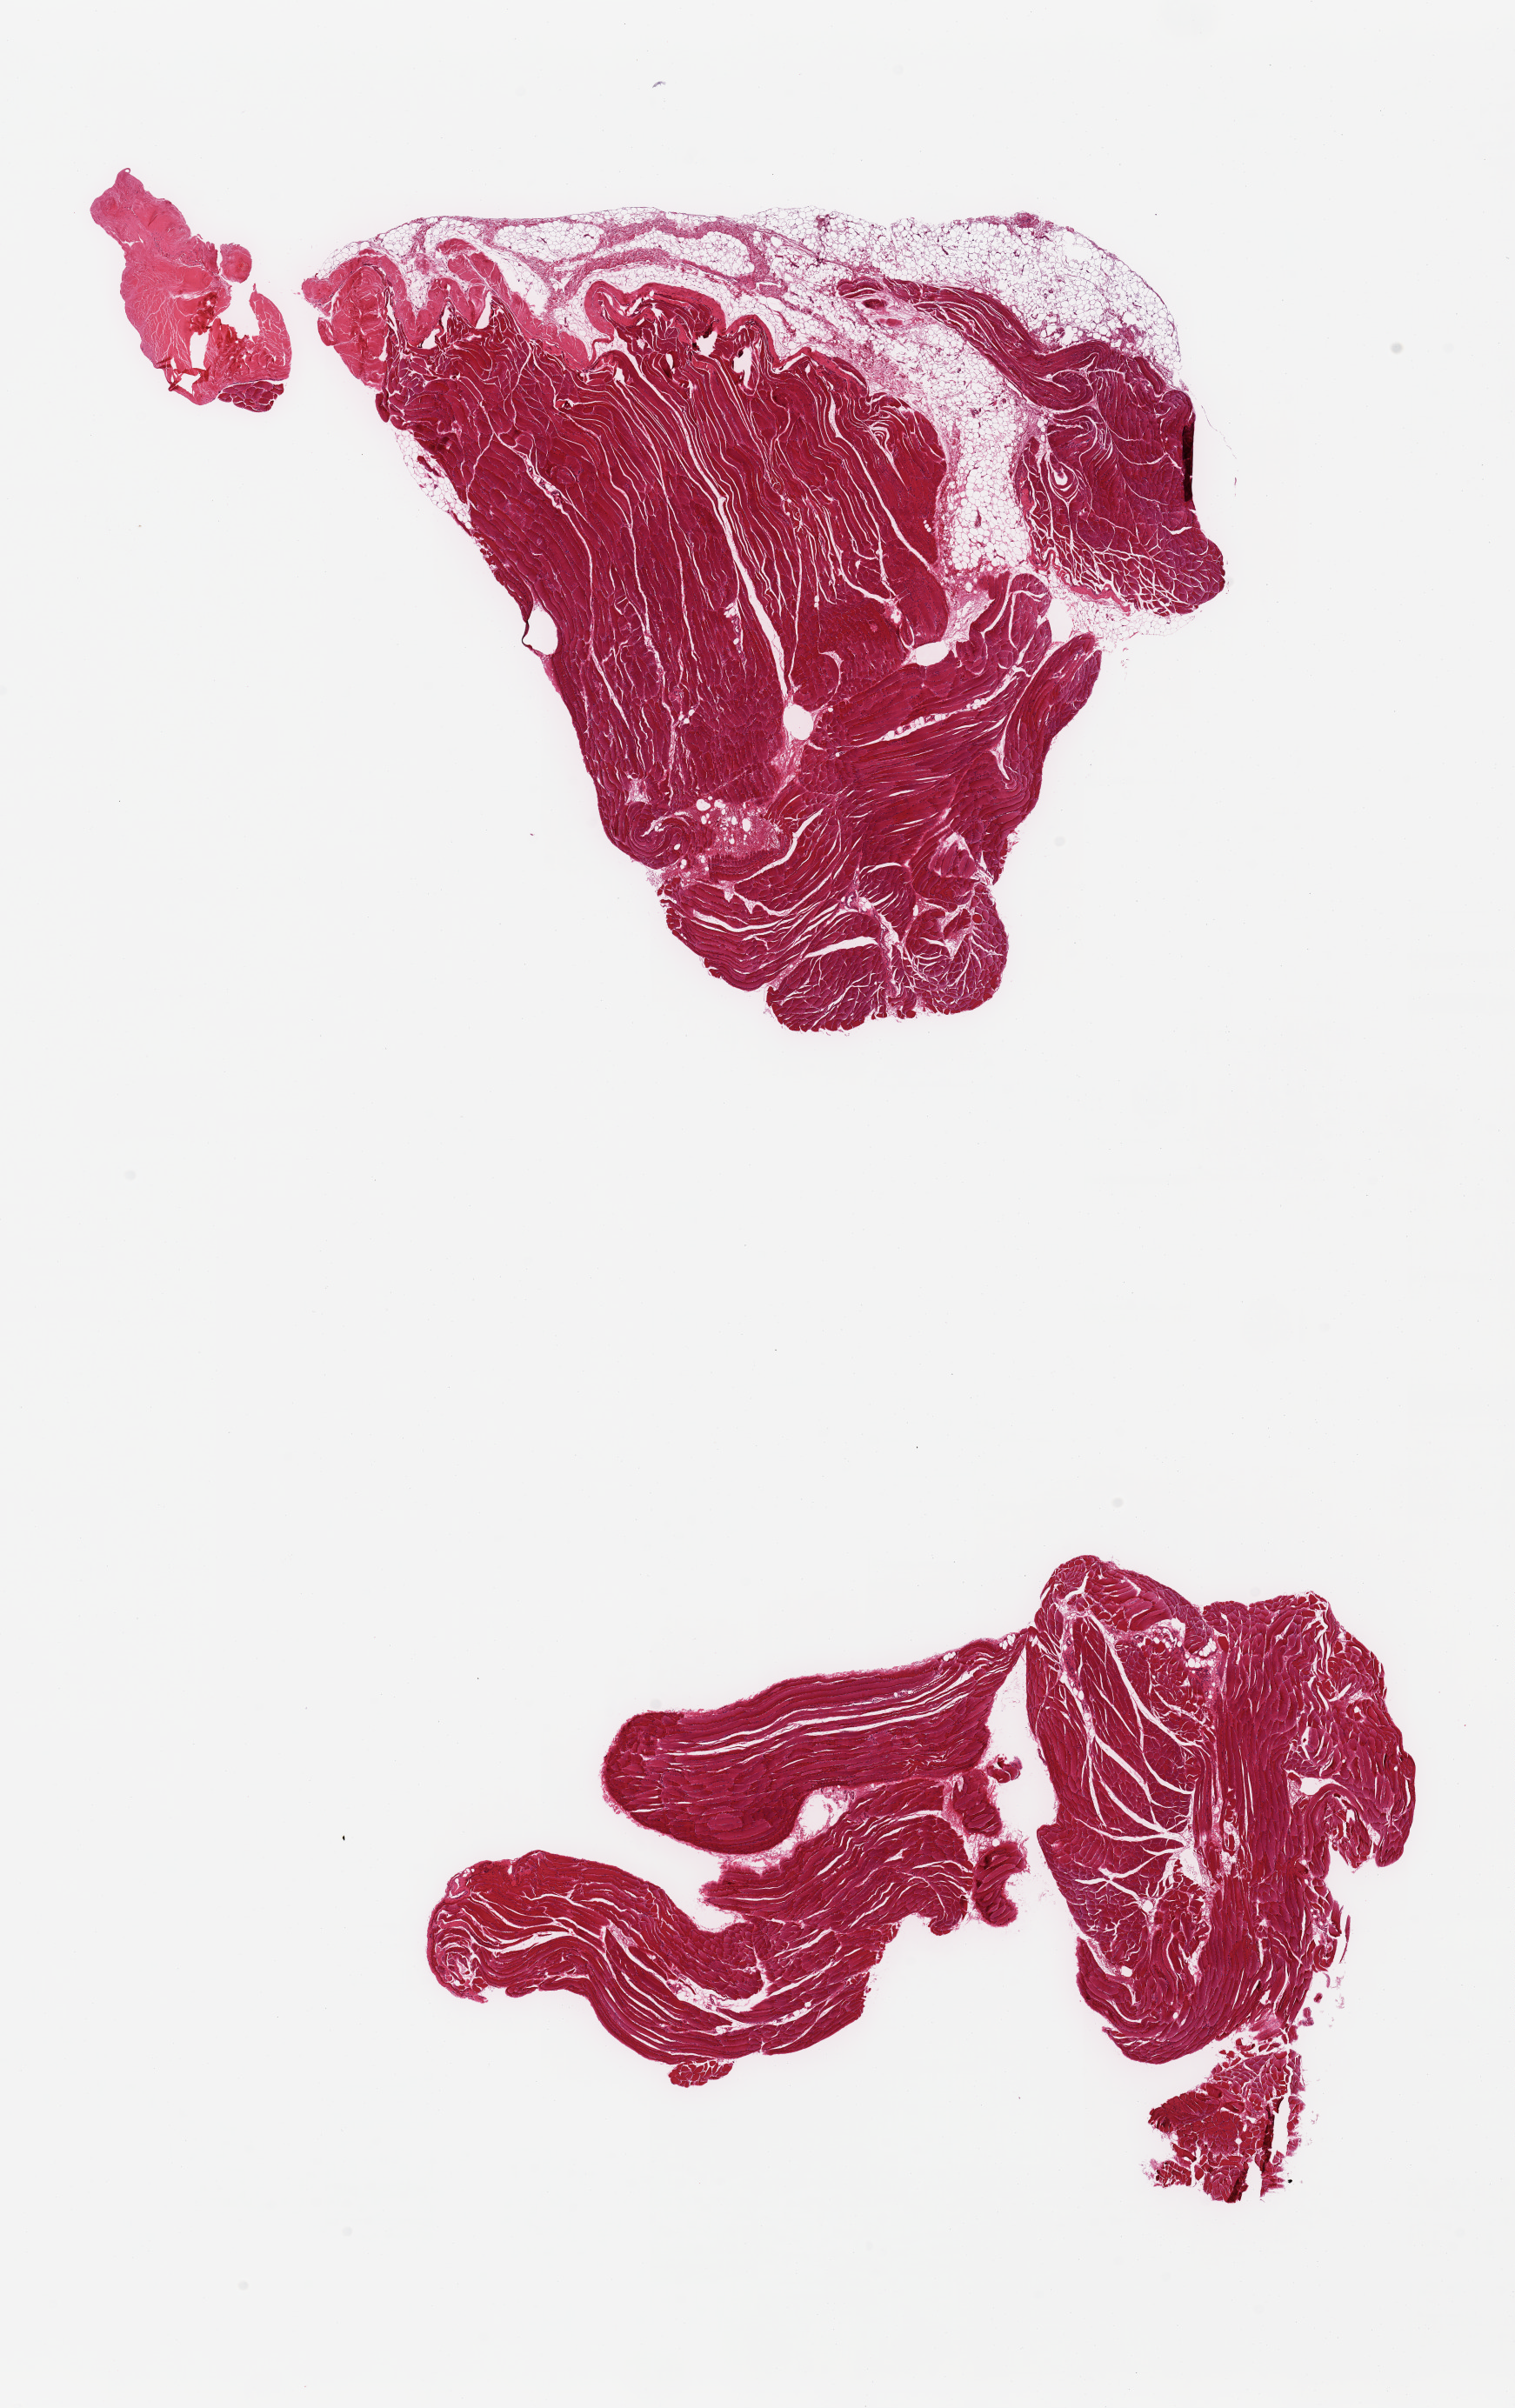
Digitized H&E-stained section, a low-resolution overview of the entire scanned area, about 13.8 x 21.9 mm, PAXgene-fixed, paraffin-embedded tissue, target tissue: skeletal muscle, tissue donor sample. Donor: female.
• pathologist's review note for this sample: 2 pieces, adherent/interstitial fat/tendon up to ~15% of tissue